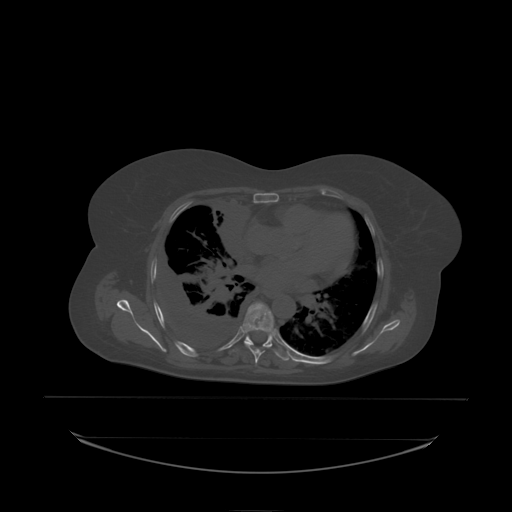
CT including the spine, one axial slice; slice 146 of 242 in the series (ordered by position); bone window (W 1800 / L 400 HU); 512 × 512 image matrix. Female patient, age 53 years. Case-level facts recorded for this patient, not image findings: primary cancer: lung; vertebrae with lytic lesions (as recorded): T7, L1.
Structures marked on this image (semi-automatic segmentation, software-assisted and operator-edited):
- T6 vertebra: box from (x=243, y=302) to (x=273, y=334) px
- T7 vertebra: (x=246, y=306)–(x=275, y=338)